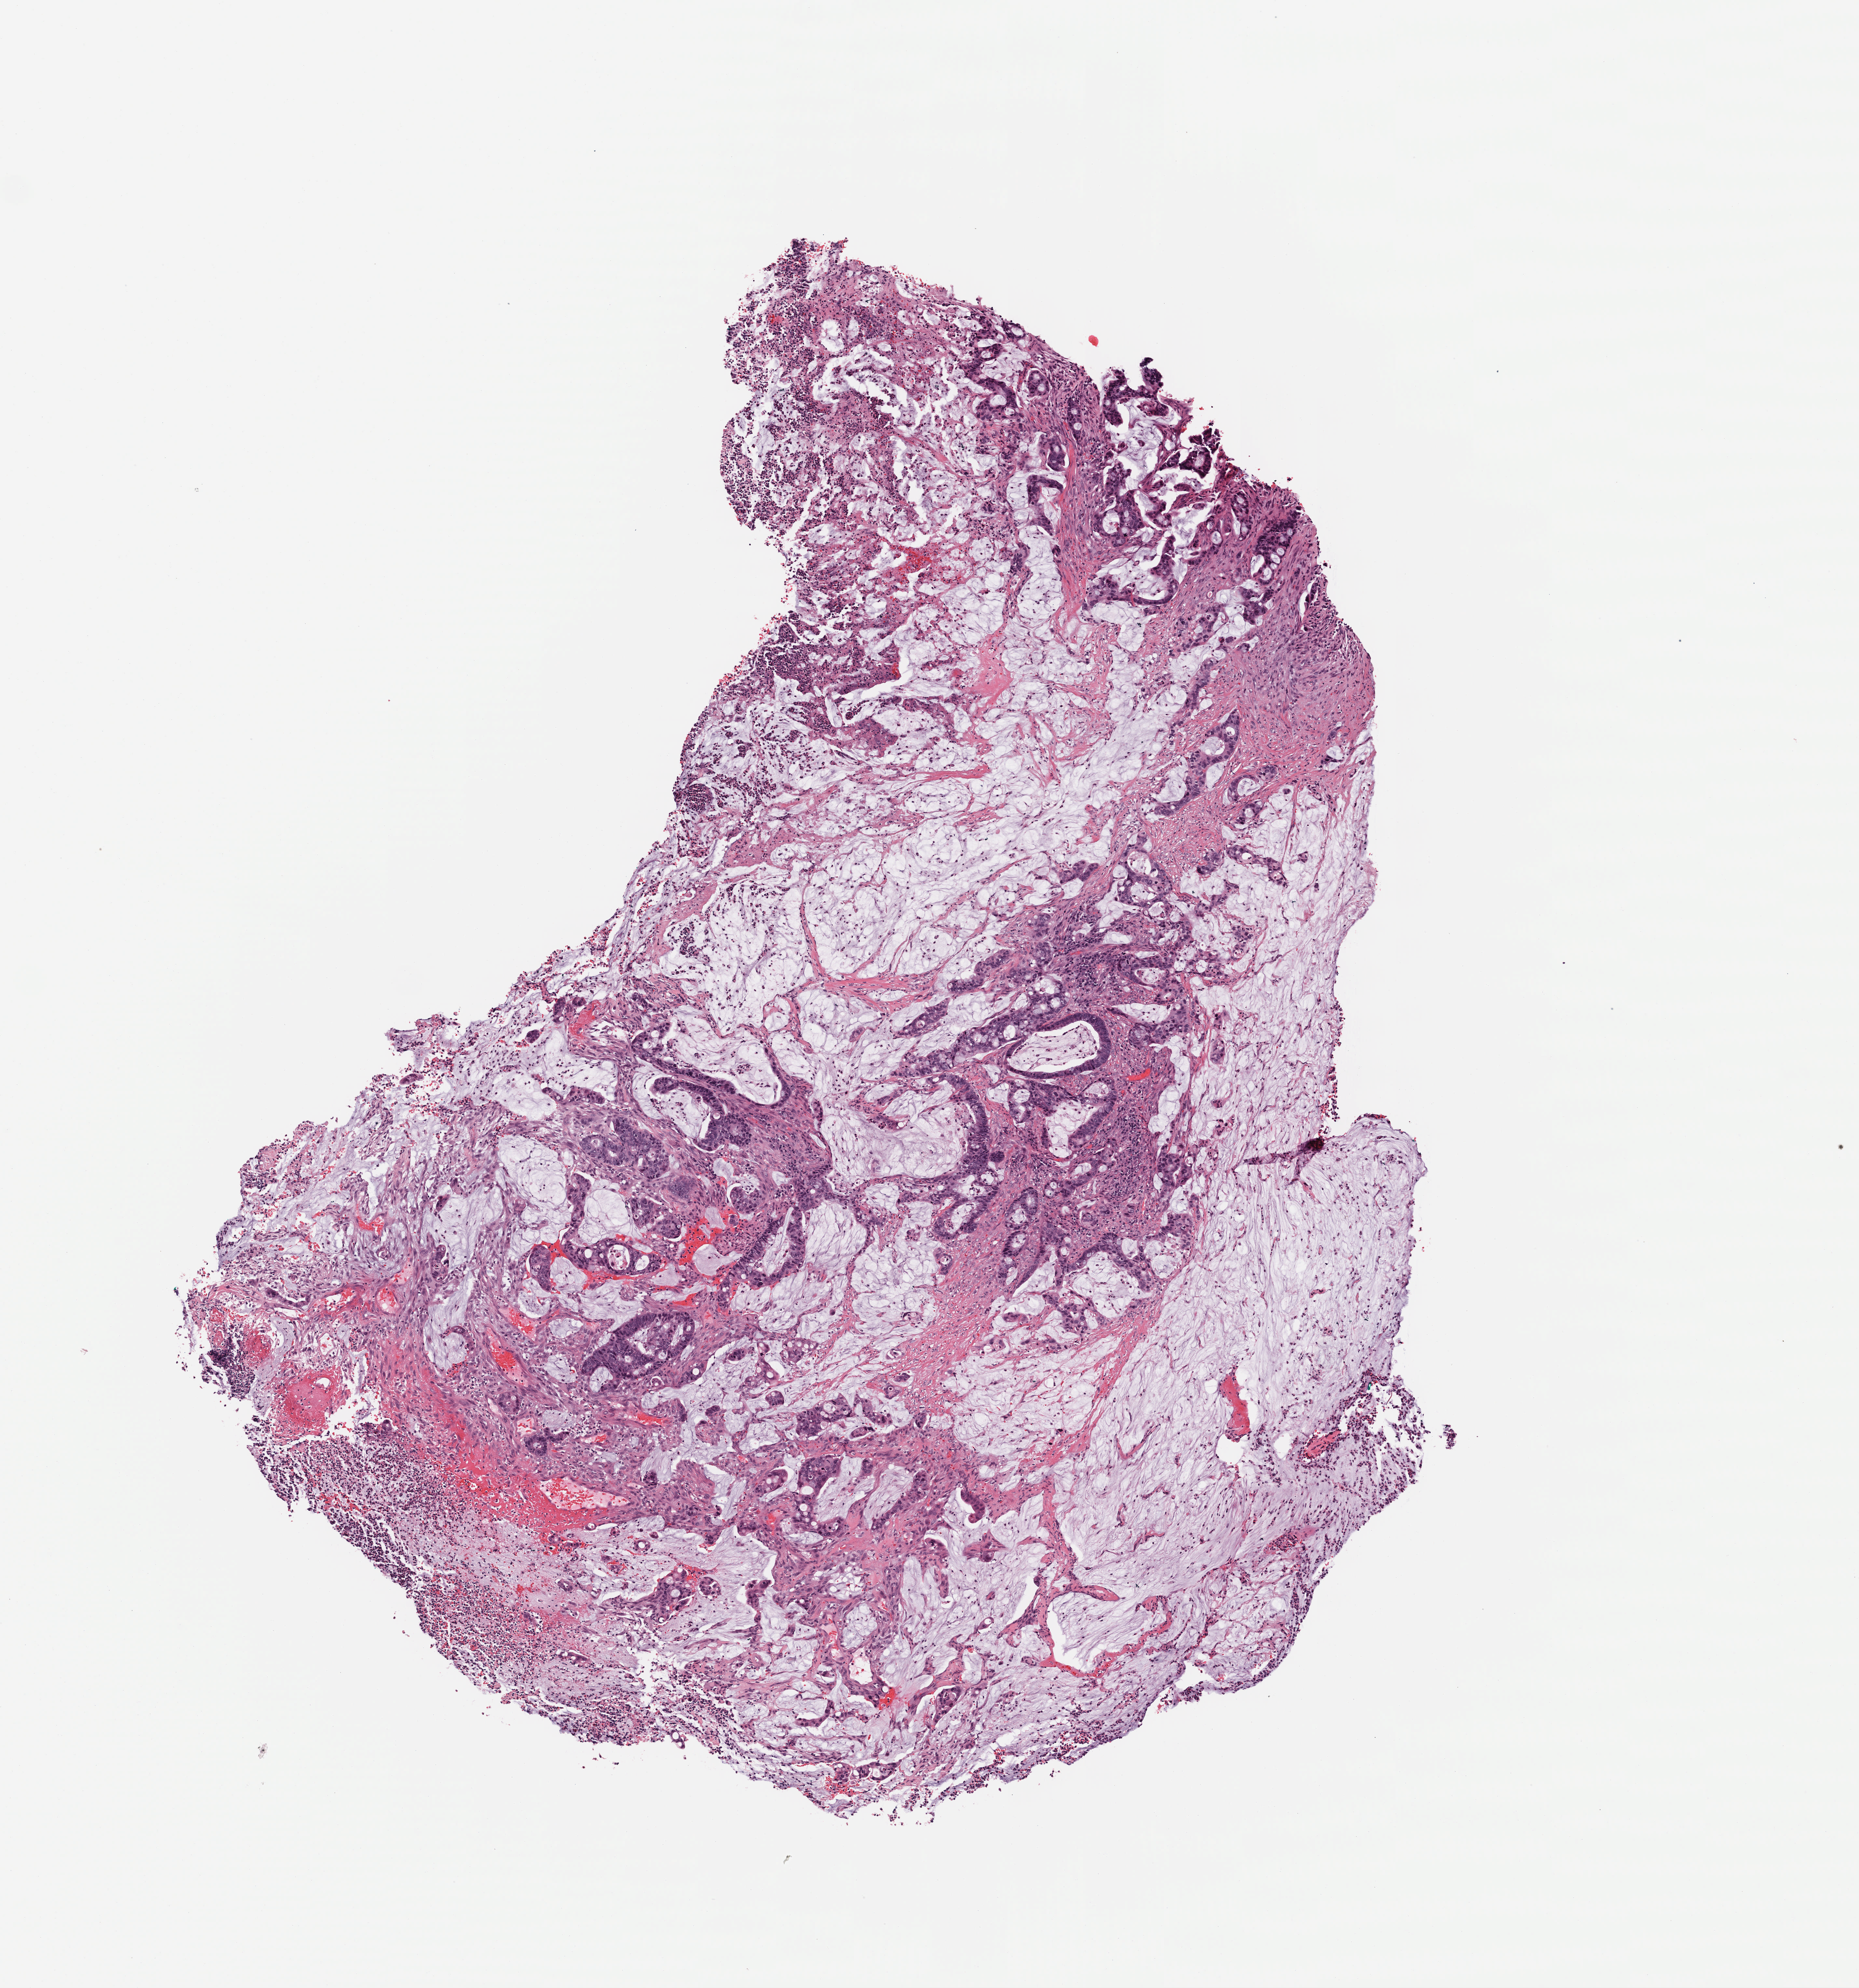
Digitized H&E tissue section (whole slide) — shown as a low-resolution overview of the whole scanned area (about 5.6 x 6.0 mm, acquisition: 40x scan); frozen section; primary tumour sample from the colon. Male patient; age at initial diagnosis 71 years. Pathologist review of this section (percent, as recorded): tumour cells 68%, tumour nuclei 65%, normal cells 0%, stromal cells 30%, necrosis 2%. Infiltration values recorded for this section: lymphocyte infiltration 6%, monocyte infiltration 3%, neutrophil infiltration 20%.
- lymph nodes positive (case pathology): 7 of 20 examined
- pathologic diagnosis: Mucinous adenocarcinoma
- AJCC pathologic stage: IV (6th edition)